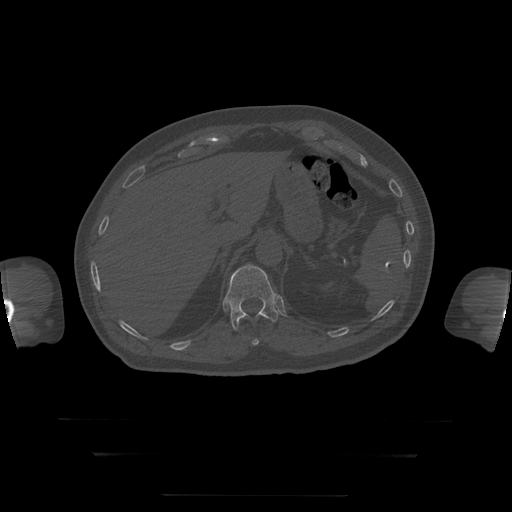
CT including the spine, one axial slice; position 81 of 397 along the scan axis; reconstruction kernel STANDARD; 120 kVp; bone window (W 1800 / L 400 HU); 1.25 mm slice thickness; 512 × 512 image matrix. Patient age 73 years. Case-level facts recorded for this patient, not image findings: primary cancer: prostate.
Structures marked on this image (semi-automatically segmented with operator editing):
- T11 vertebra: bounding box (x1, y1, x2, y2) in pixels: (252, 339, 259, 346)
- T12 vertebra: (225, 265, 279, 330)